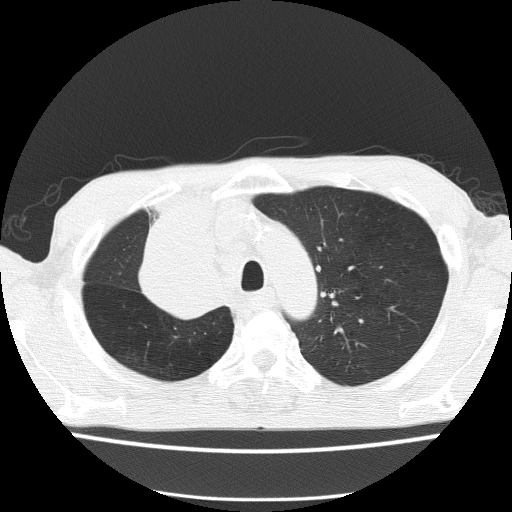
Low-dose screening chest CT, one axial slice. Slice 116 of 150 in the series (ordered by position). Reconstruction kernel FC51. Lung window (W 1500 / L -600 HU). 2 mm slice thickness. 512 × 512 image matrix, field of view 336 × 336 mm.
Outlined on this slice (outlined manually by an expert reader):
- lesion 1 (tumor, hilum of right lung): bounding box (x1, y1, x2, y2) in pixels: (141, 194, 218, 317)